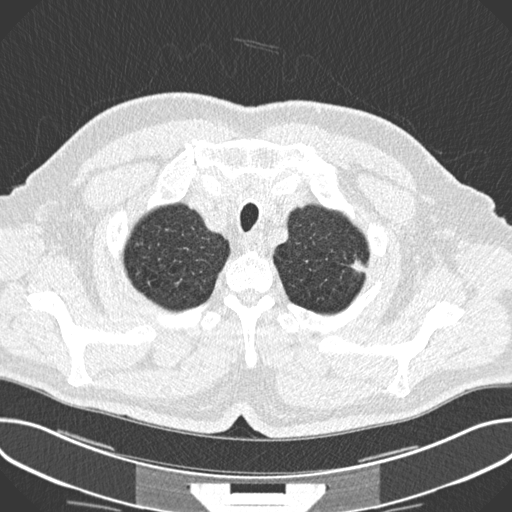
Axial slice from a low-dose chest CT screening exam, baseline annual screen, lung window (W 1500 / L -600 HU), 120 kVp, slice 26 of 245 in the series, 512 × 512 image matrix, field of view 380 × 380 mm. Male, age 63 years at enrolment. Current smoker at enrolment.
• Lesion marked by an expert reader, bounding box [x1, y1, x2, y2] px = [342, 250, 382, 282].
• The screening reader recorded 2 non-calcified nodules or masses ≥4 mm on this exam (left upper lobe, left upper lobe); which of them this box marks is not recorded.